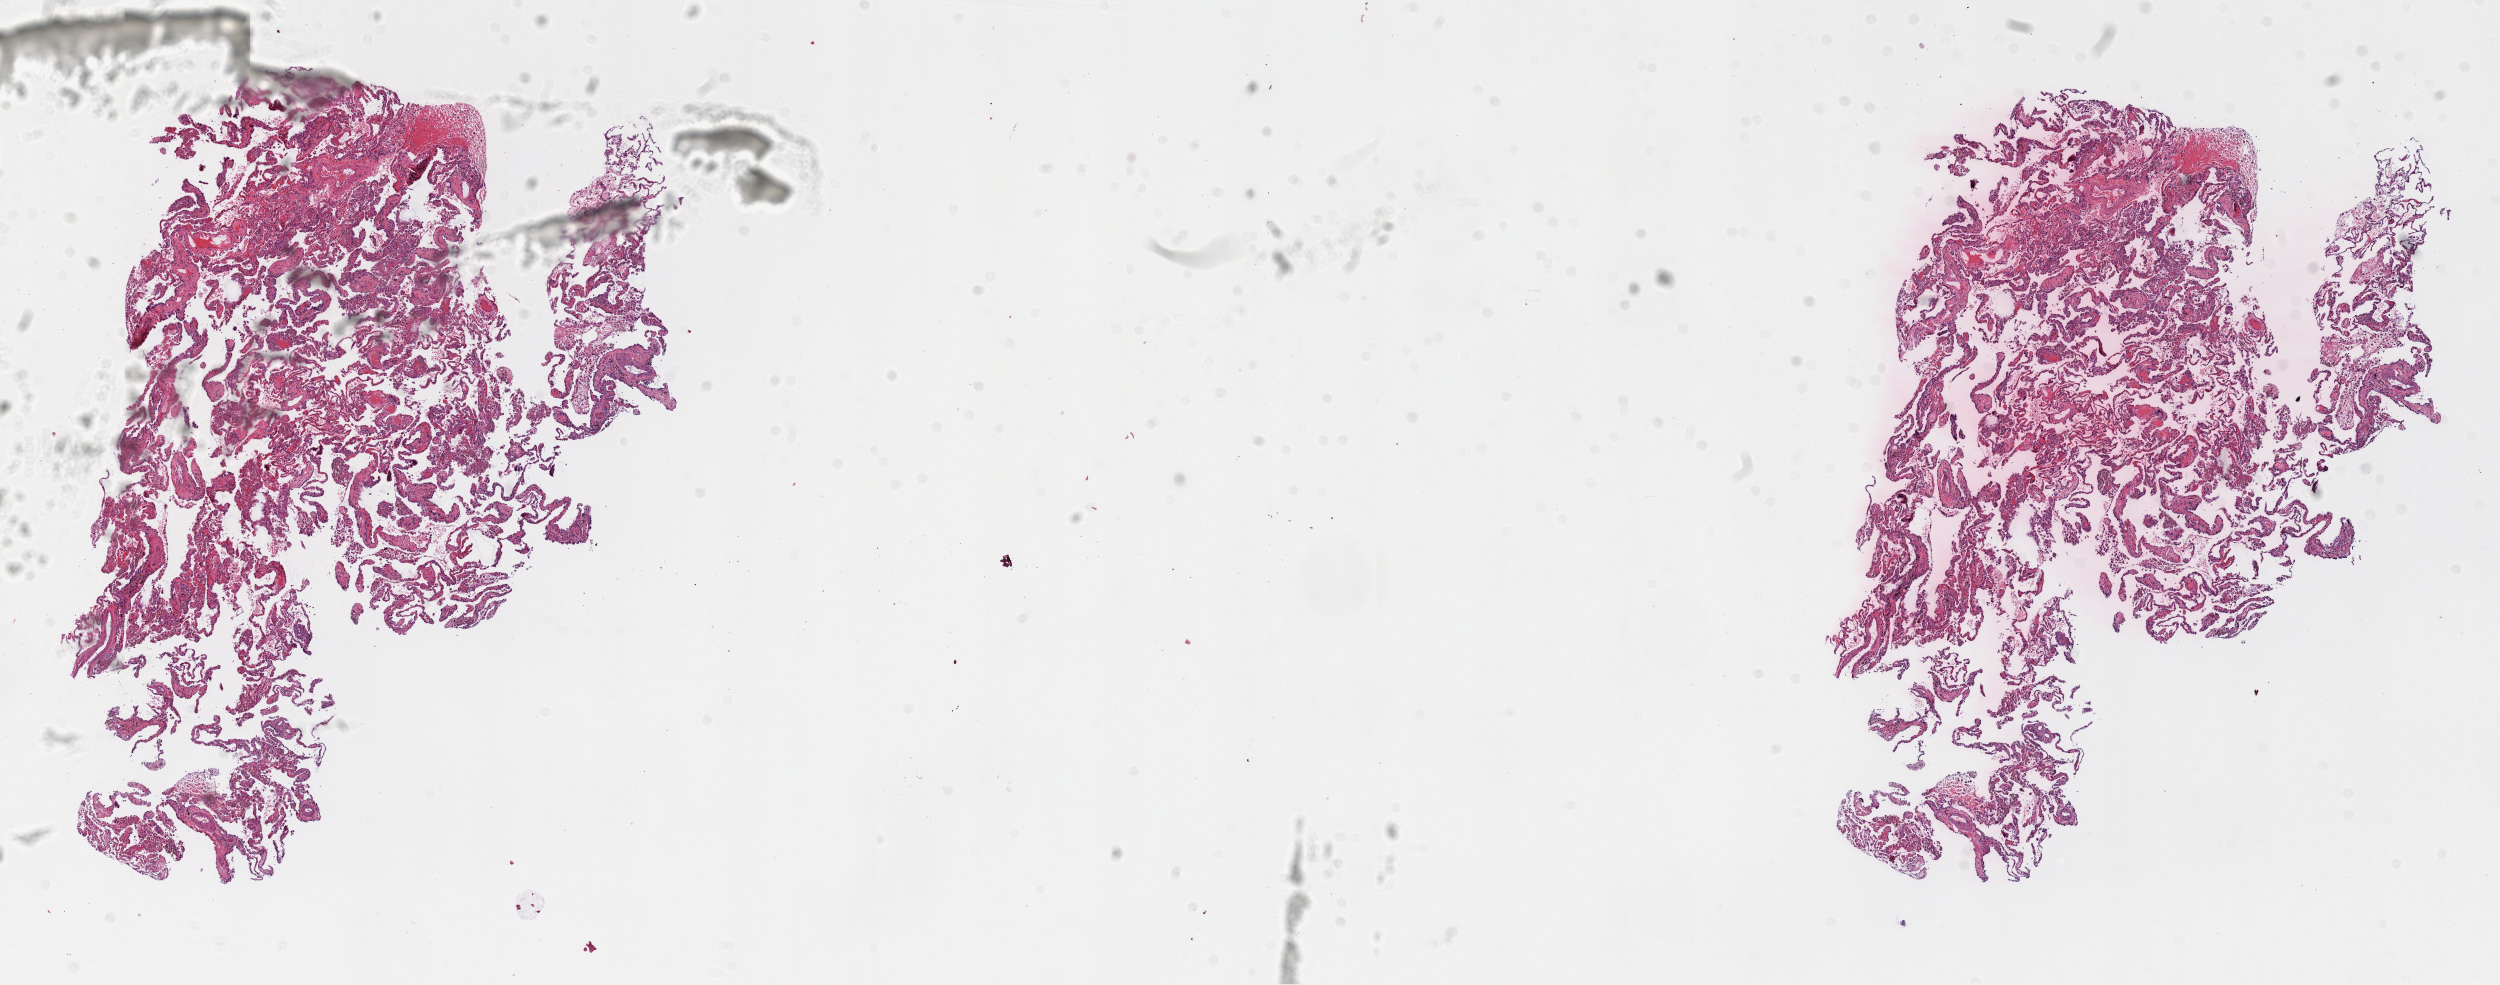
Digitized H&E tissue section (whole slide) — low-resolution overview of the scanned area, about 20.1 x 7.9 mm (acquisition: 20x scan). Frozen section from the top of the tissue portion. Lung, solid tissue normal (non-tumour tissue) sample. Female, age 47 years at initial diagnosis.
This section: solid tissue normal sample (biorepository sample class). Patient diagnosis: Squamous cell carcinoma, NOS.